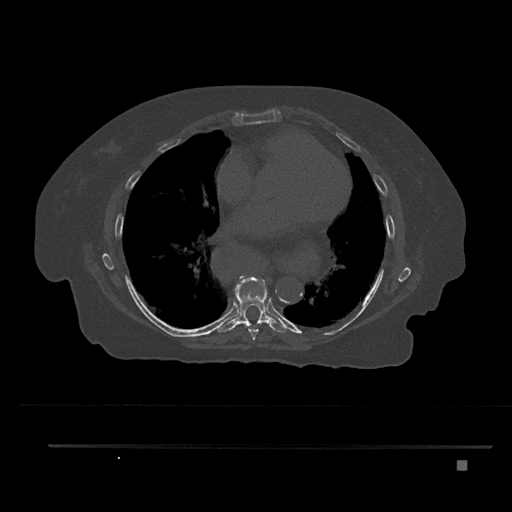
CT including the spine, one axial slice; slice 459 of 797 in the series (ordered by position); reconstruction kernel Br40s/3; bone window (W 1800 / L 400 HU); 0.5 mm slice thickness; 512 × 512 image matrix, field of view 437 × 437 mm. Patient: female, 76 years. From the clinical record (not read from this slice): primary cancer: lung; vertebrae with lytic lesions (as recorded): T11, L3.
Outlined on this slice (semi-automatically segmented with operator editing):
- T7 vertebra: bounding box [x1, y1, x2, y2] px = [248, 281, 262, 340]
- T8 vertebra: [218, 277, 288, 333]